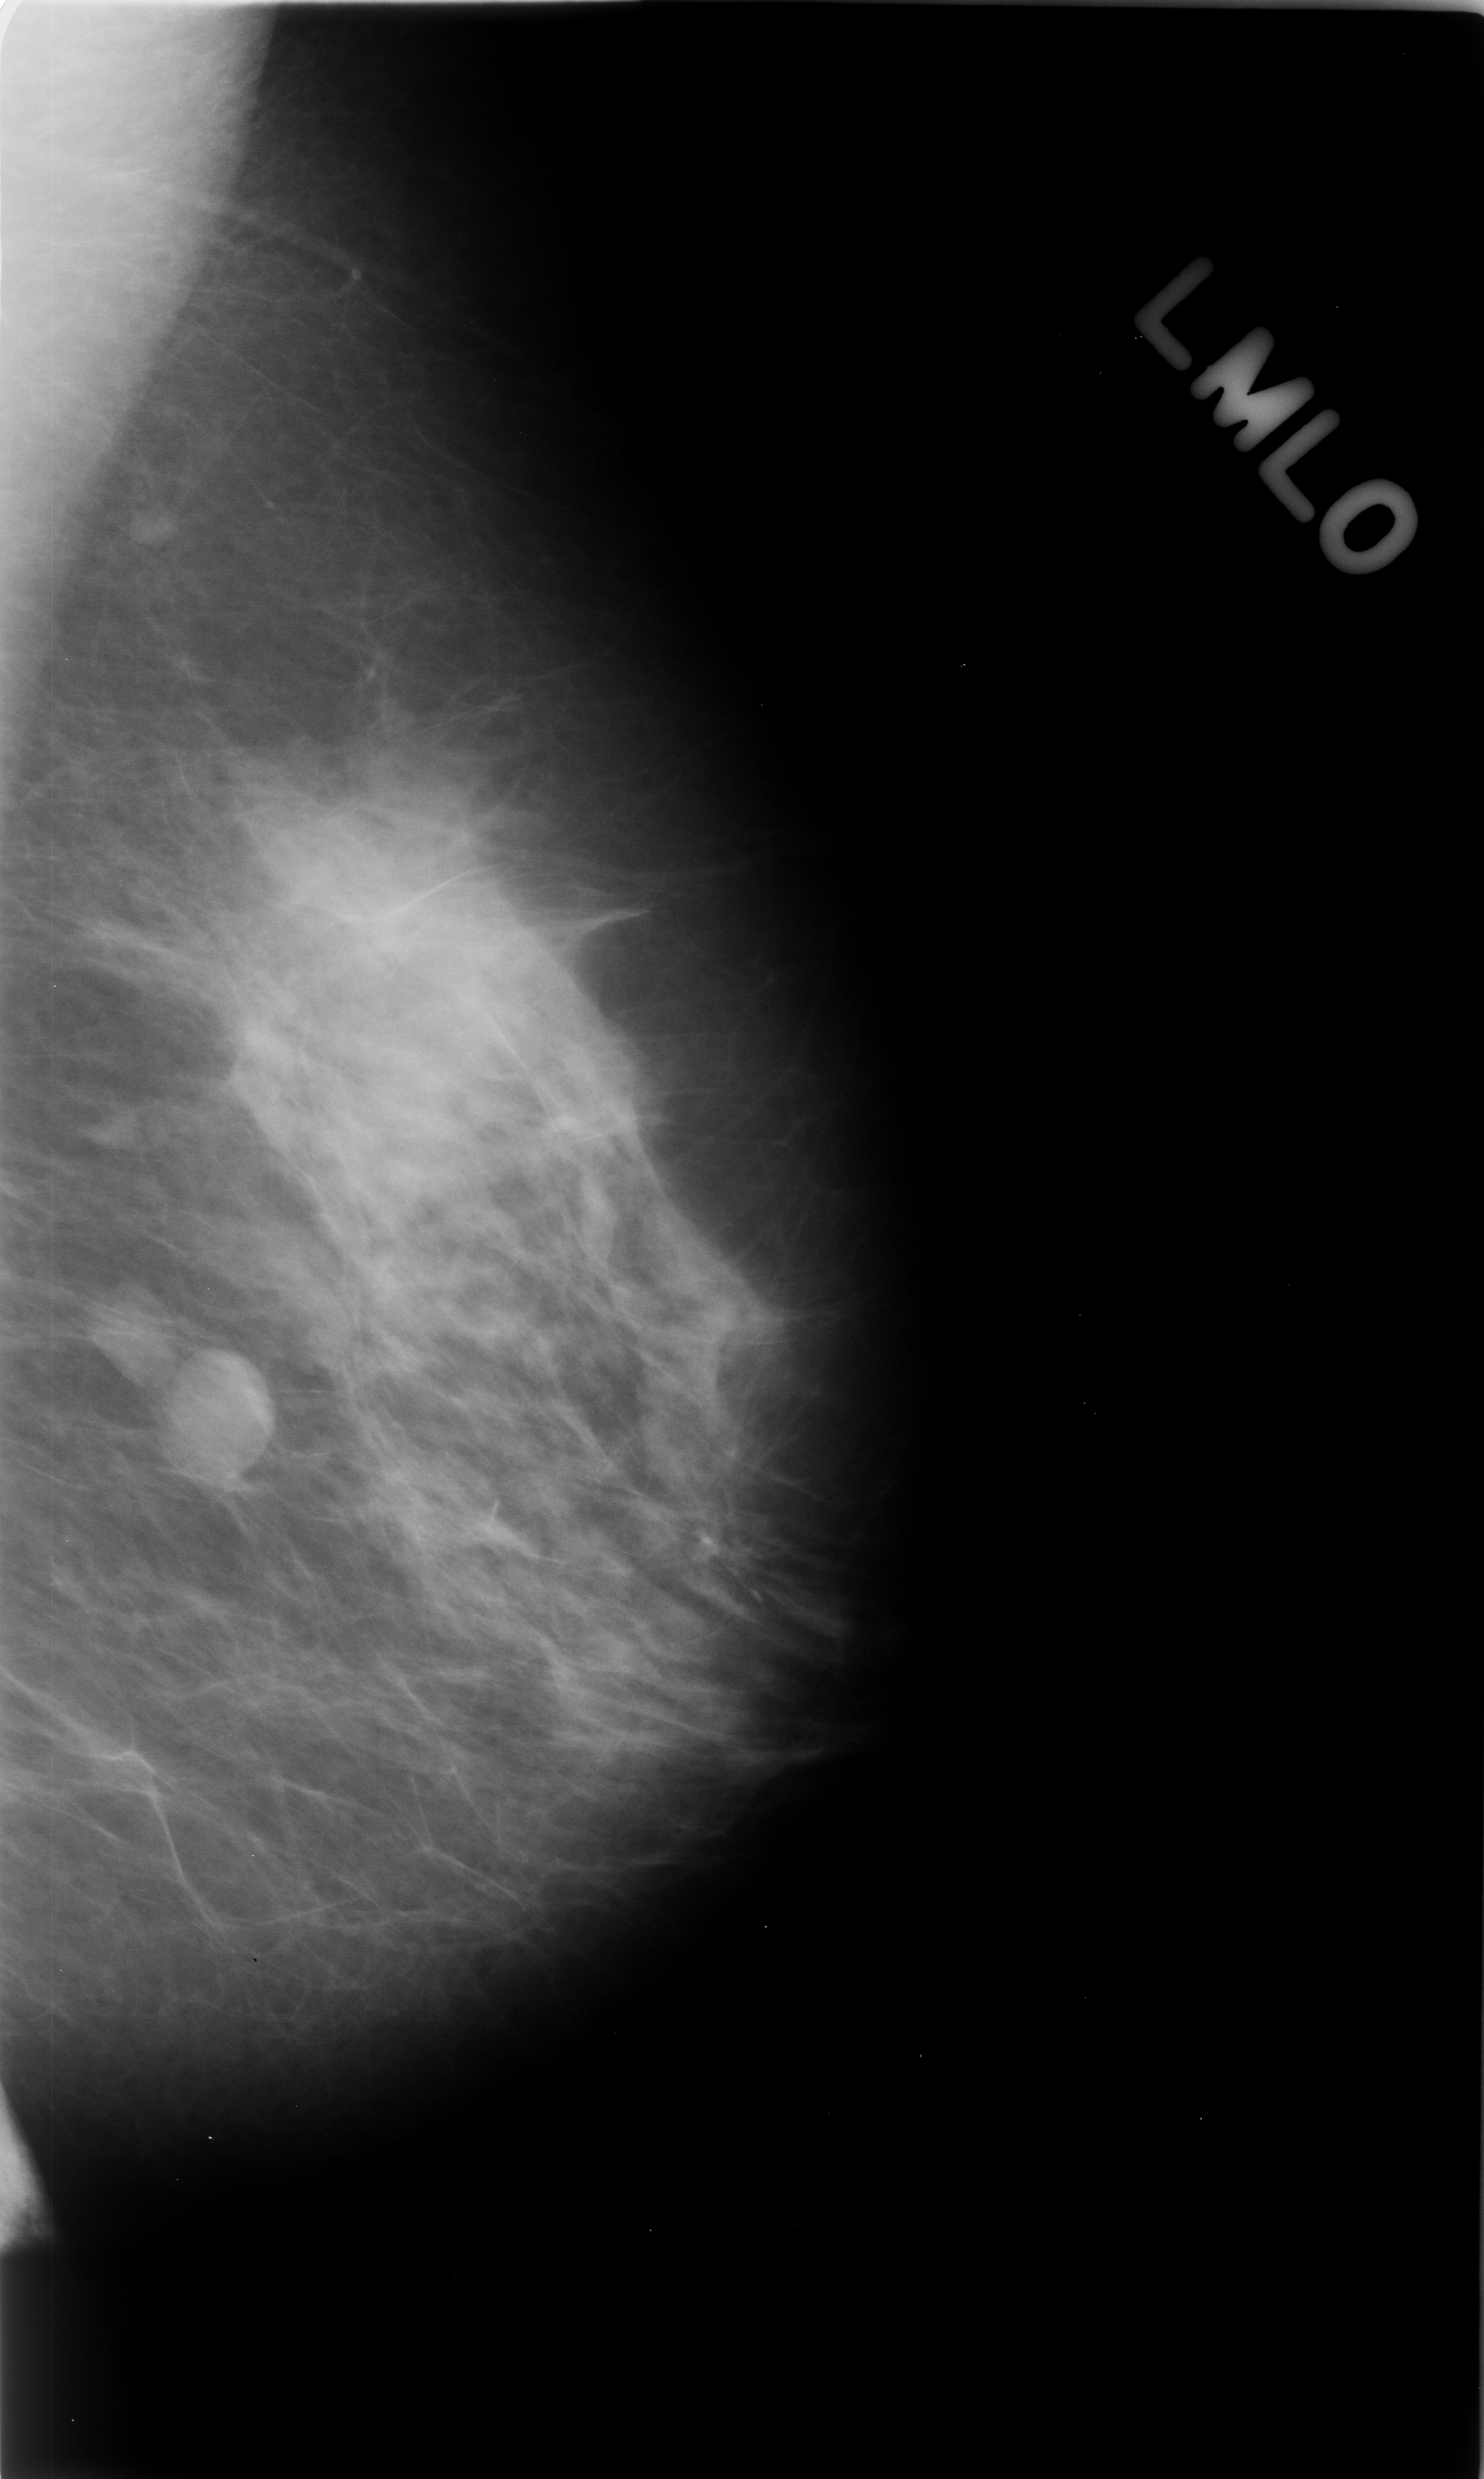
Mammogram (digitized film), left breast, mediolateral oblique (MLO) view, breast composition: scattered fibroglandular densities (BI-RADS density category 2 of 4).
- Abnormality record for this image: Finding 1 of 2: mass, shape oval, margins circumscribed; BI-RADS assessment category 3; pathology result (as recorded, not read from the image): benign.
- Finding 2 of 2: mass, shape oval, margins circumscribed; BI-RADS assessment category 3; pathology result (as recorded, not read from the image): benign.